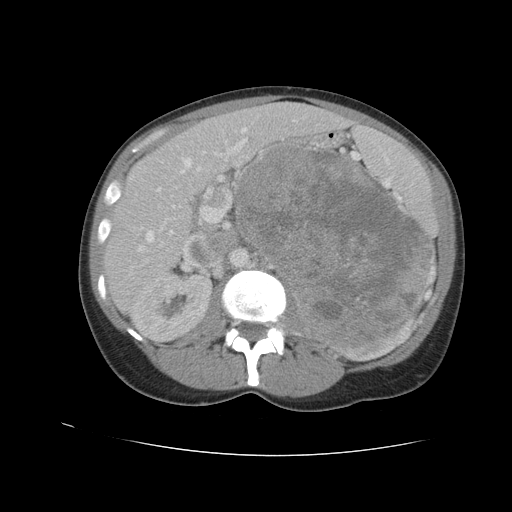
Contrast-enhanced abdominal CT, one axial slice; position 61 of 90 along the scan axis; reconstruction kernel STANDARD; intravenous contrast given; soft-tissue window (W 400 / L 40 HU); 5 mm slice thickness; 512 × 512 image matrix, field of view 360 × 360 mm. Female patient. From the clinical record (not read from this slice): diagnosis: adrenocortical carcinoma; tumour side: left adrenal; tumour size at pathology: 18 cm; Ki-67 index: 11 %; stage (as recorded): 3.
Outlined on this slice (semi-automatically segmented with operator editing):
- mass: bounding box <238,145,429,344> (left, top, right, bottom; pixels)